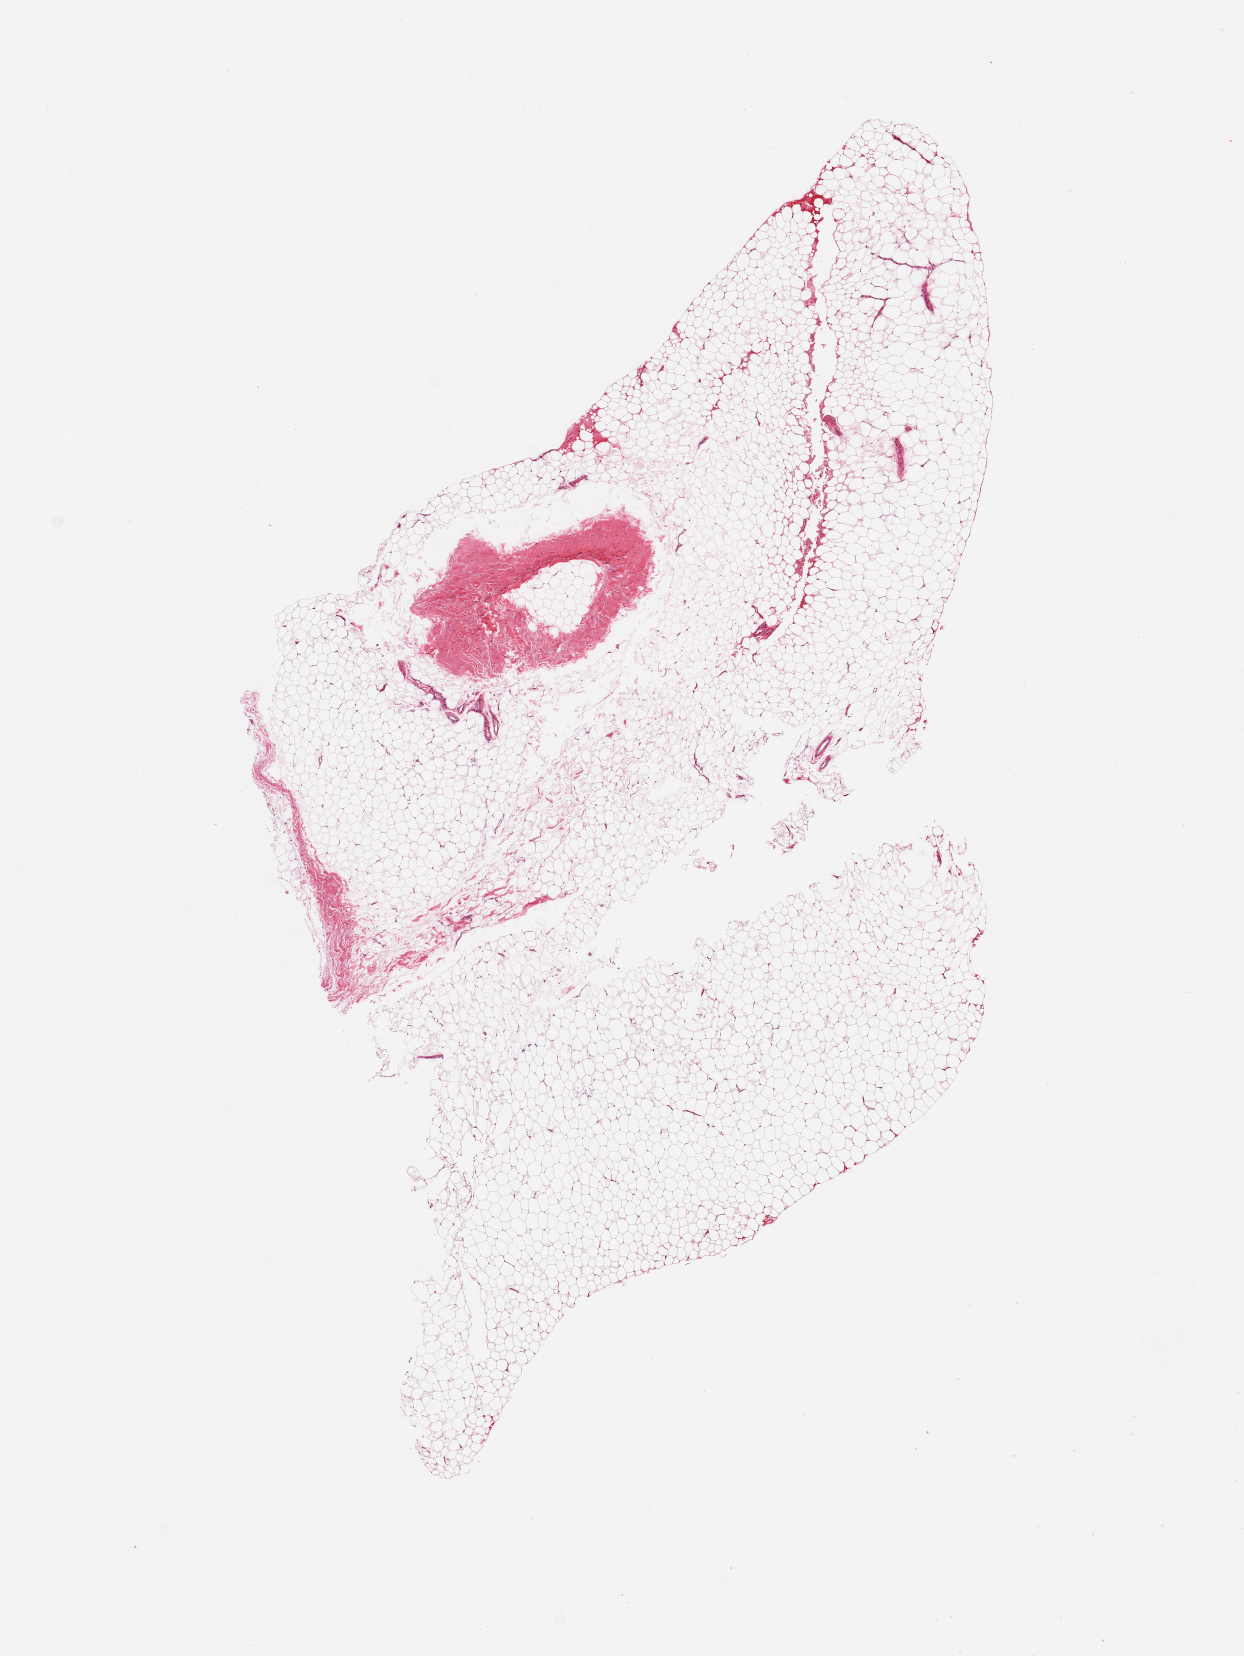
Whole-slide image, H&E stain, shown as a low-resolution overview of the whole scanned area (about 9.8 x 13.1 mm); PAXgene-fixed, paraffin-embedded tissue; target tissue: adipose tissue; tissue donor sample.
Review note (as recorded): 1 piece; not skin, adipose tissue with small portion of fibrous tissue.